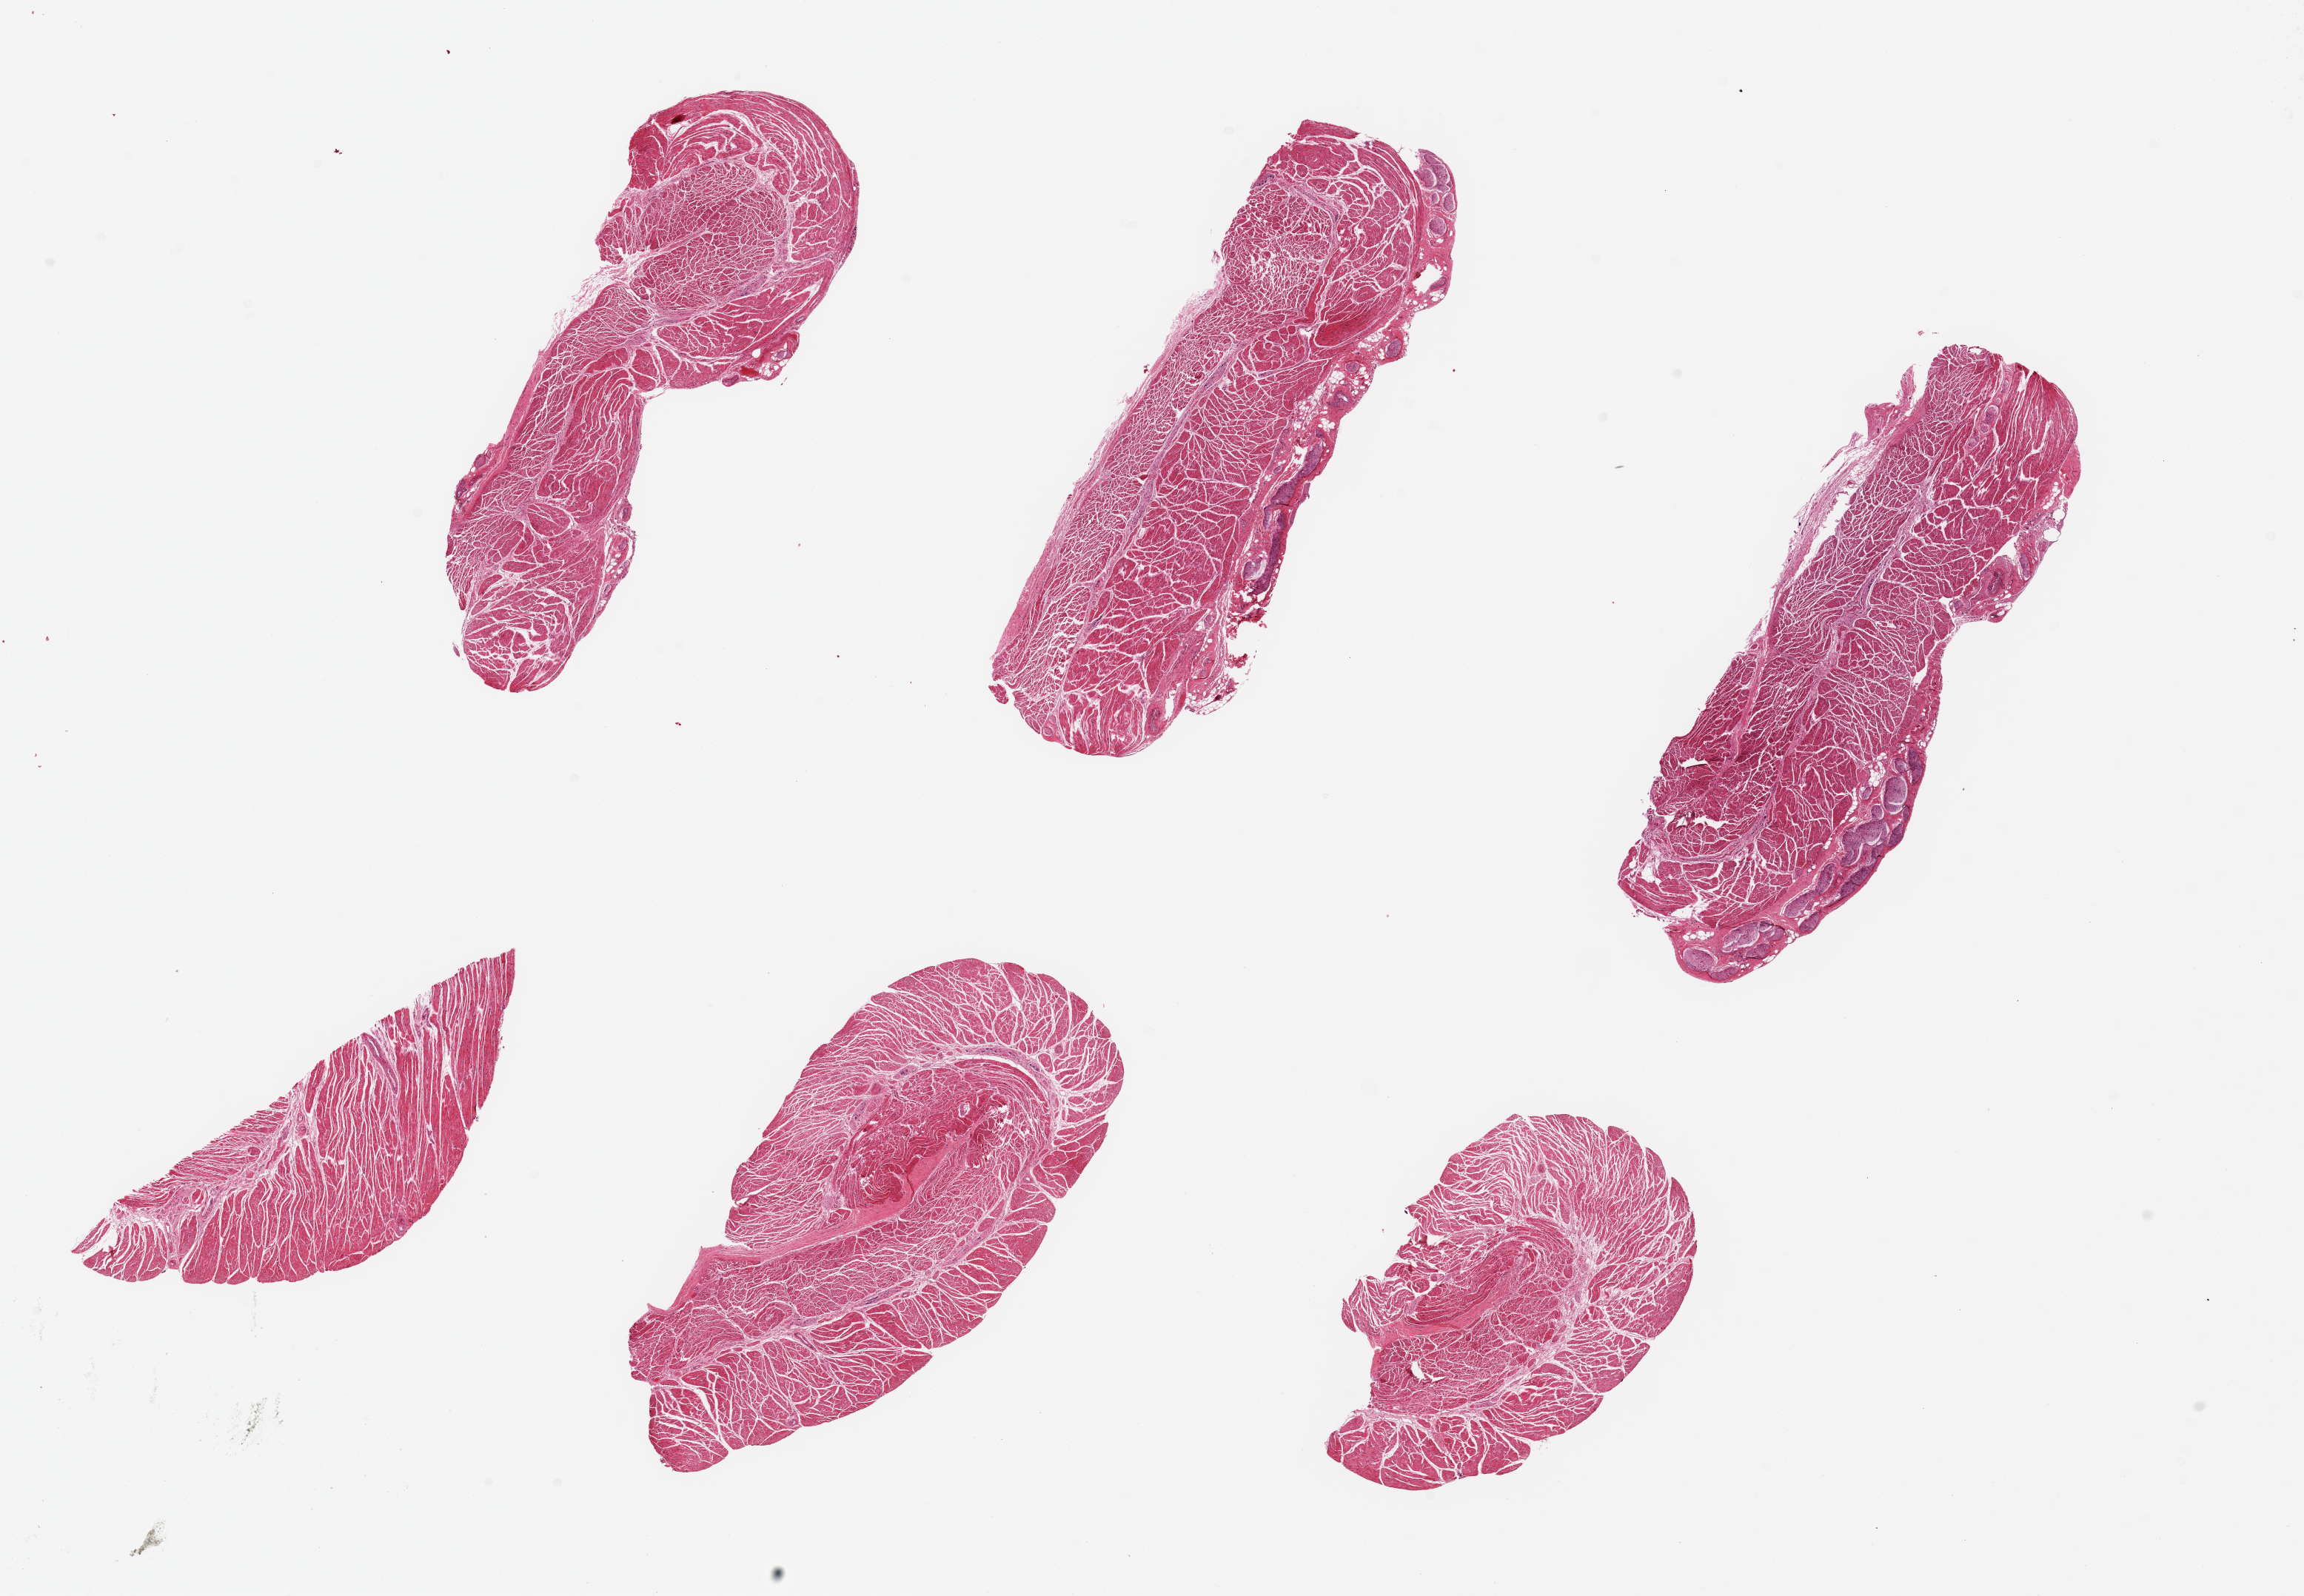
Digitized haematoxylin and eosin-stained section — shown as a low-resolution overview of the whole scanned area (about 24.6 x 17.1 mm, from a 20x scan), PAXgene-fixed paraffin-embedded (PFPE) section, target tissue: esophageal muscle, donor tissue sample. Donor: female.
Review note (as recorded): 6 pieces, up to 7x2.5mm; no extraneous tissue.